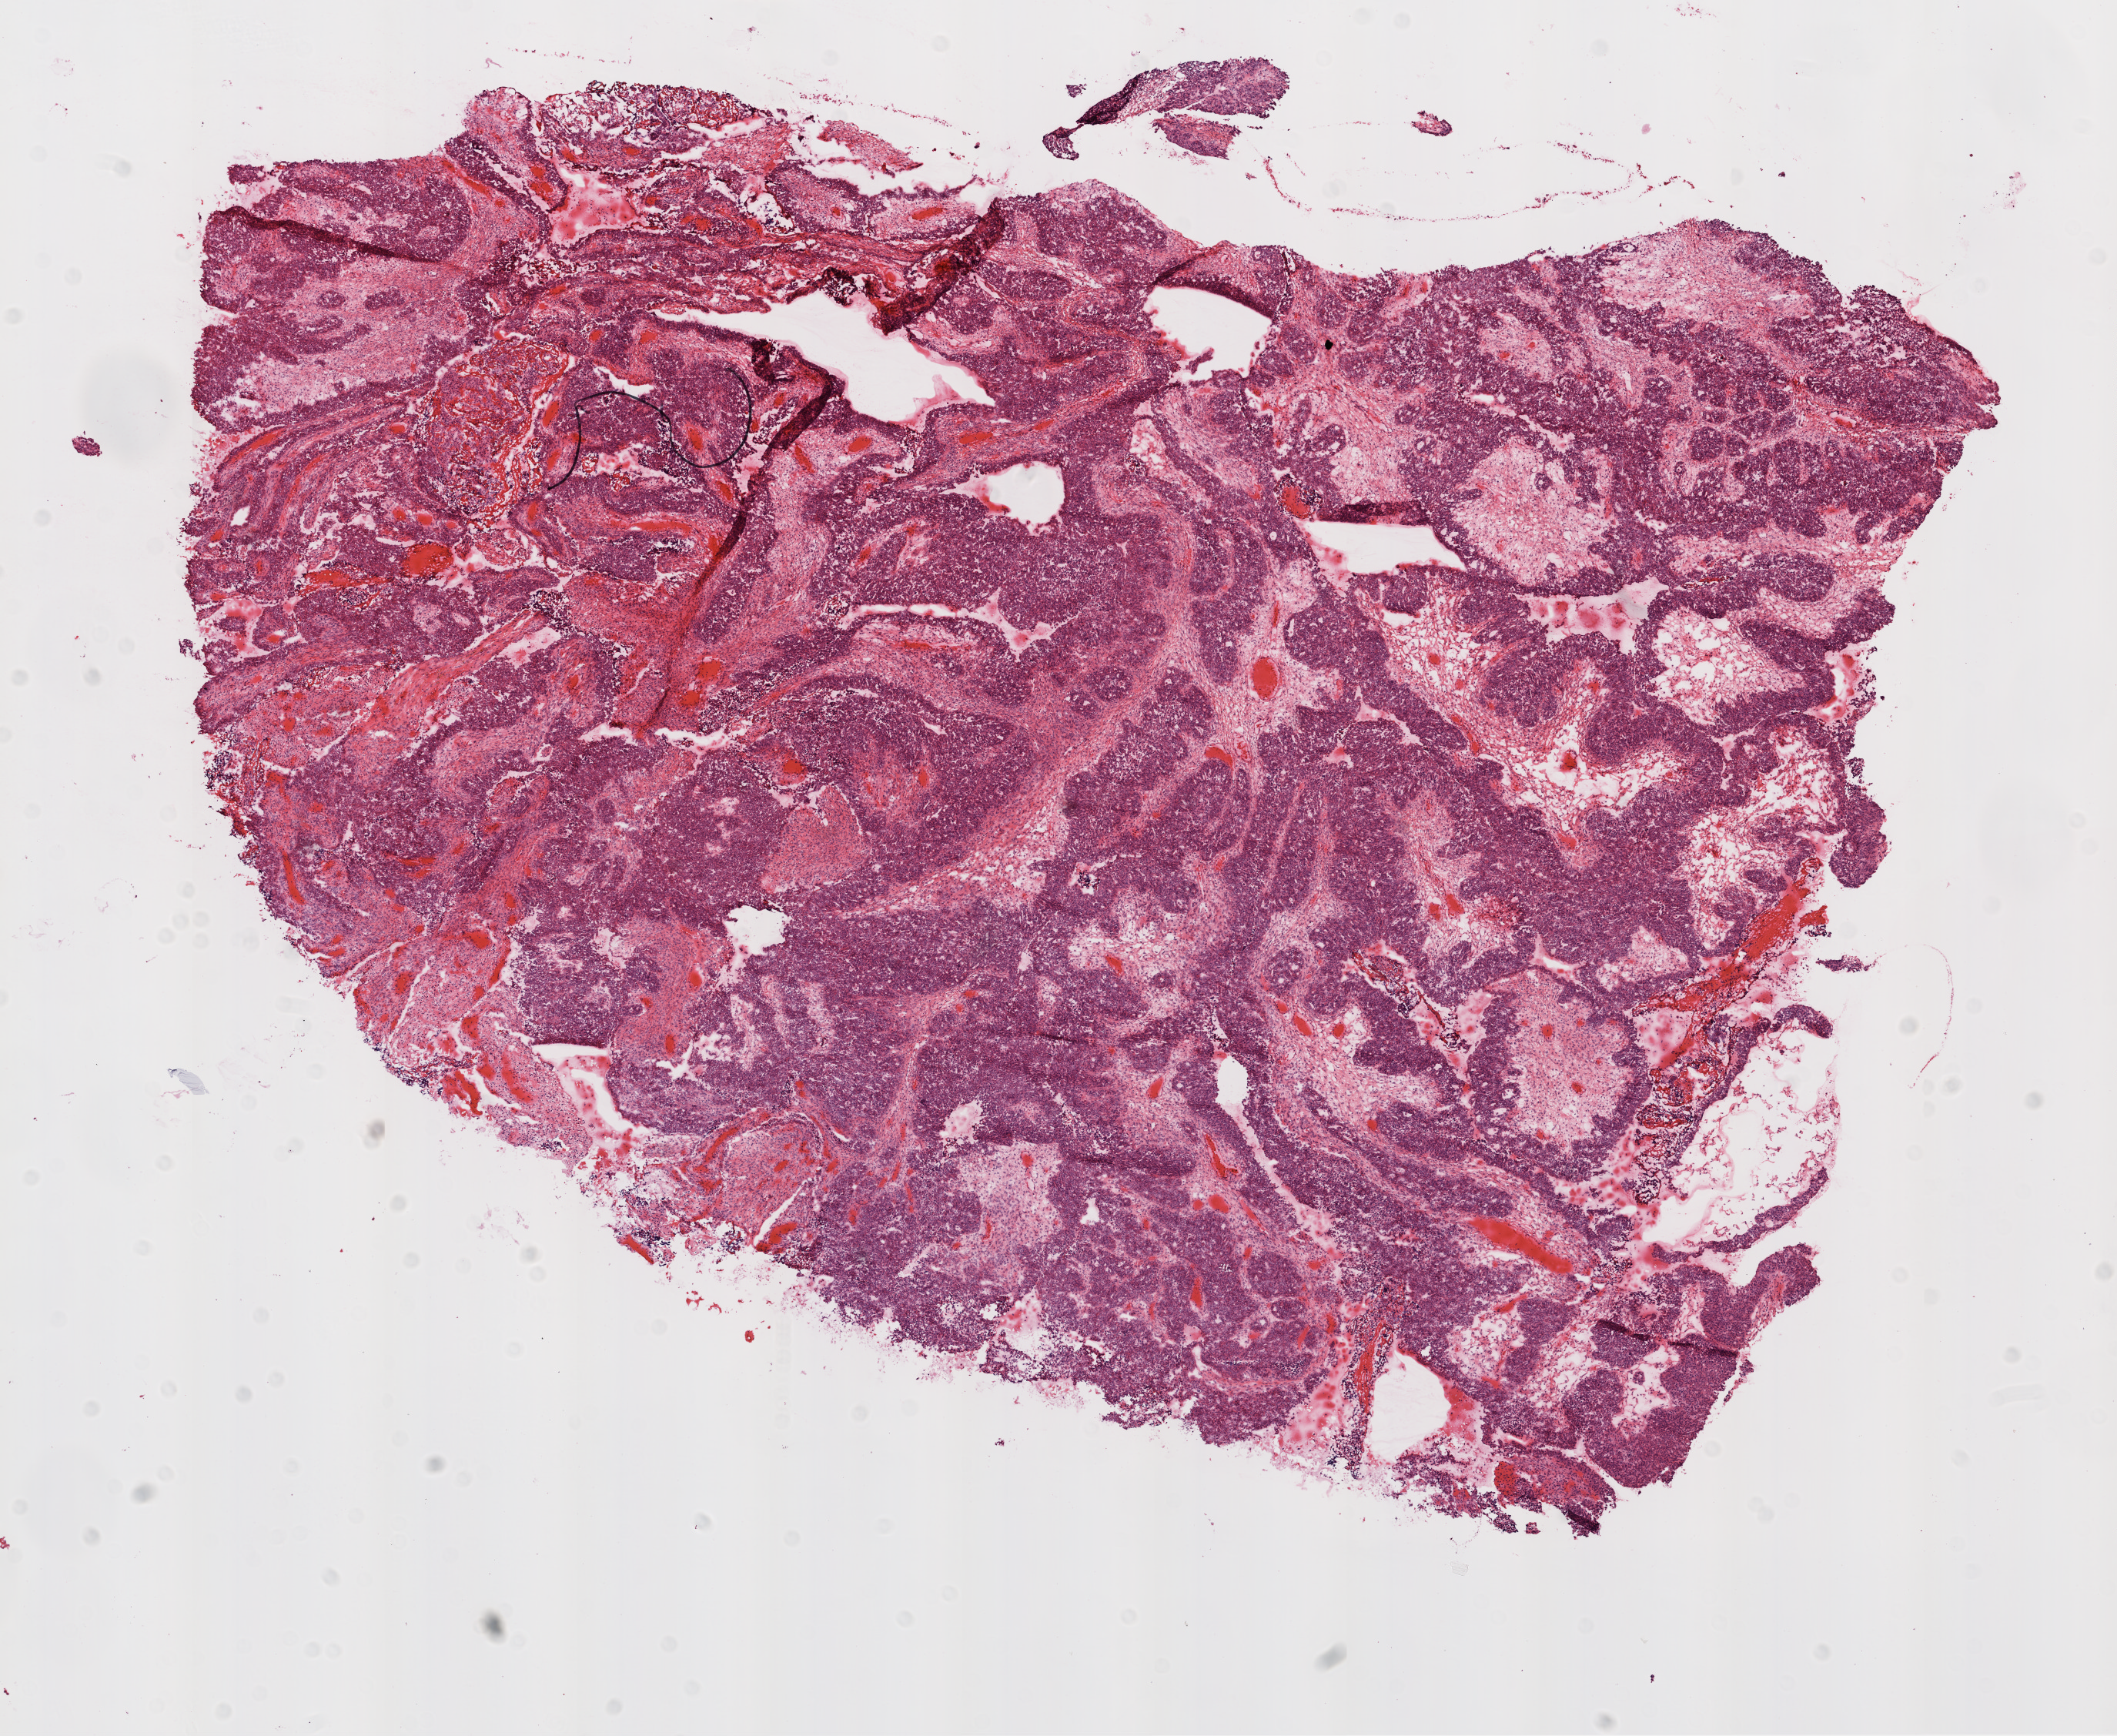
Digitized Hematoxylin and eosin (H&E) stained tissue section (whole slide) — whole scanned area (about 11.0 x 9.0 mm, slide scanned at 20x) shown as a low-resolution overview. Frozen section. Sample: primary tumour, ovary. Patient: female, age at initial diagnosis 45 years. Histologic grade: G3 (poorly differentiated). Composition of this section per pathologist review: tumour cells 70%, tumour nuclei 95%, normal cells 0%, stromal cells 30%, necrosis 0%.
- pathologic diagnosis: Serous cystadenocarcinoma, NOS
- laterality: bilateral
- FIGO stage: IIIC